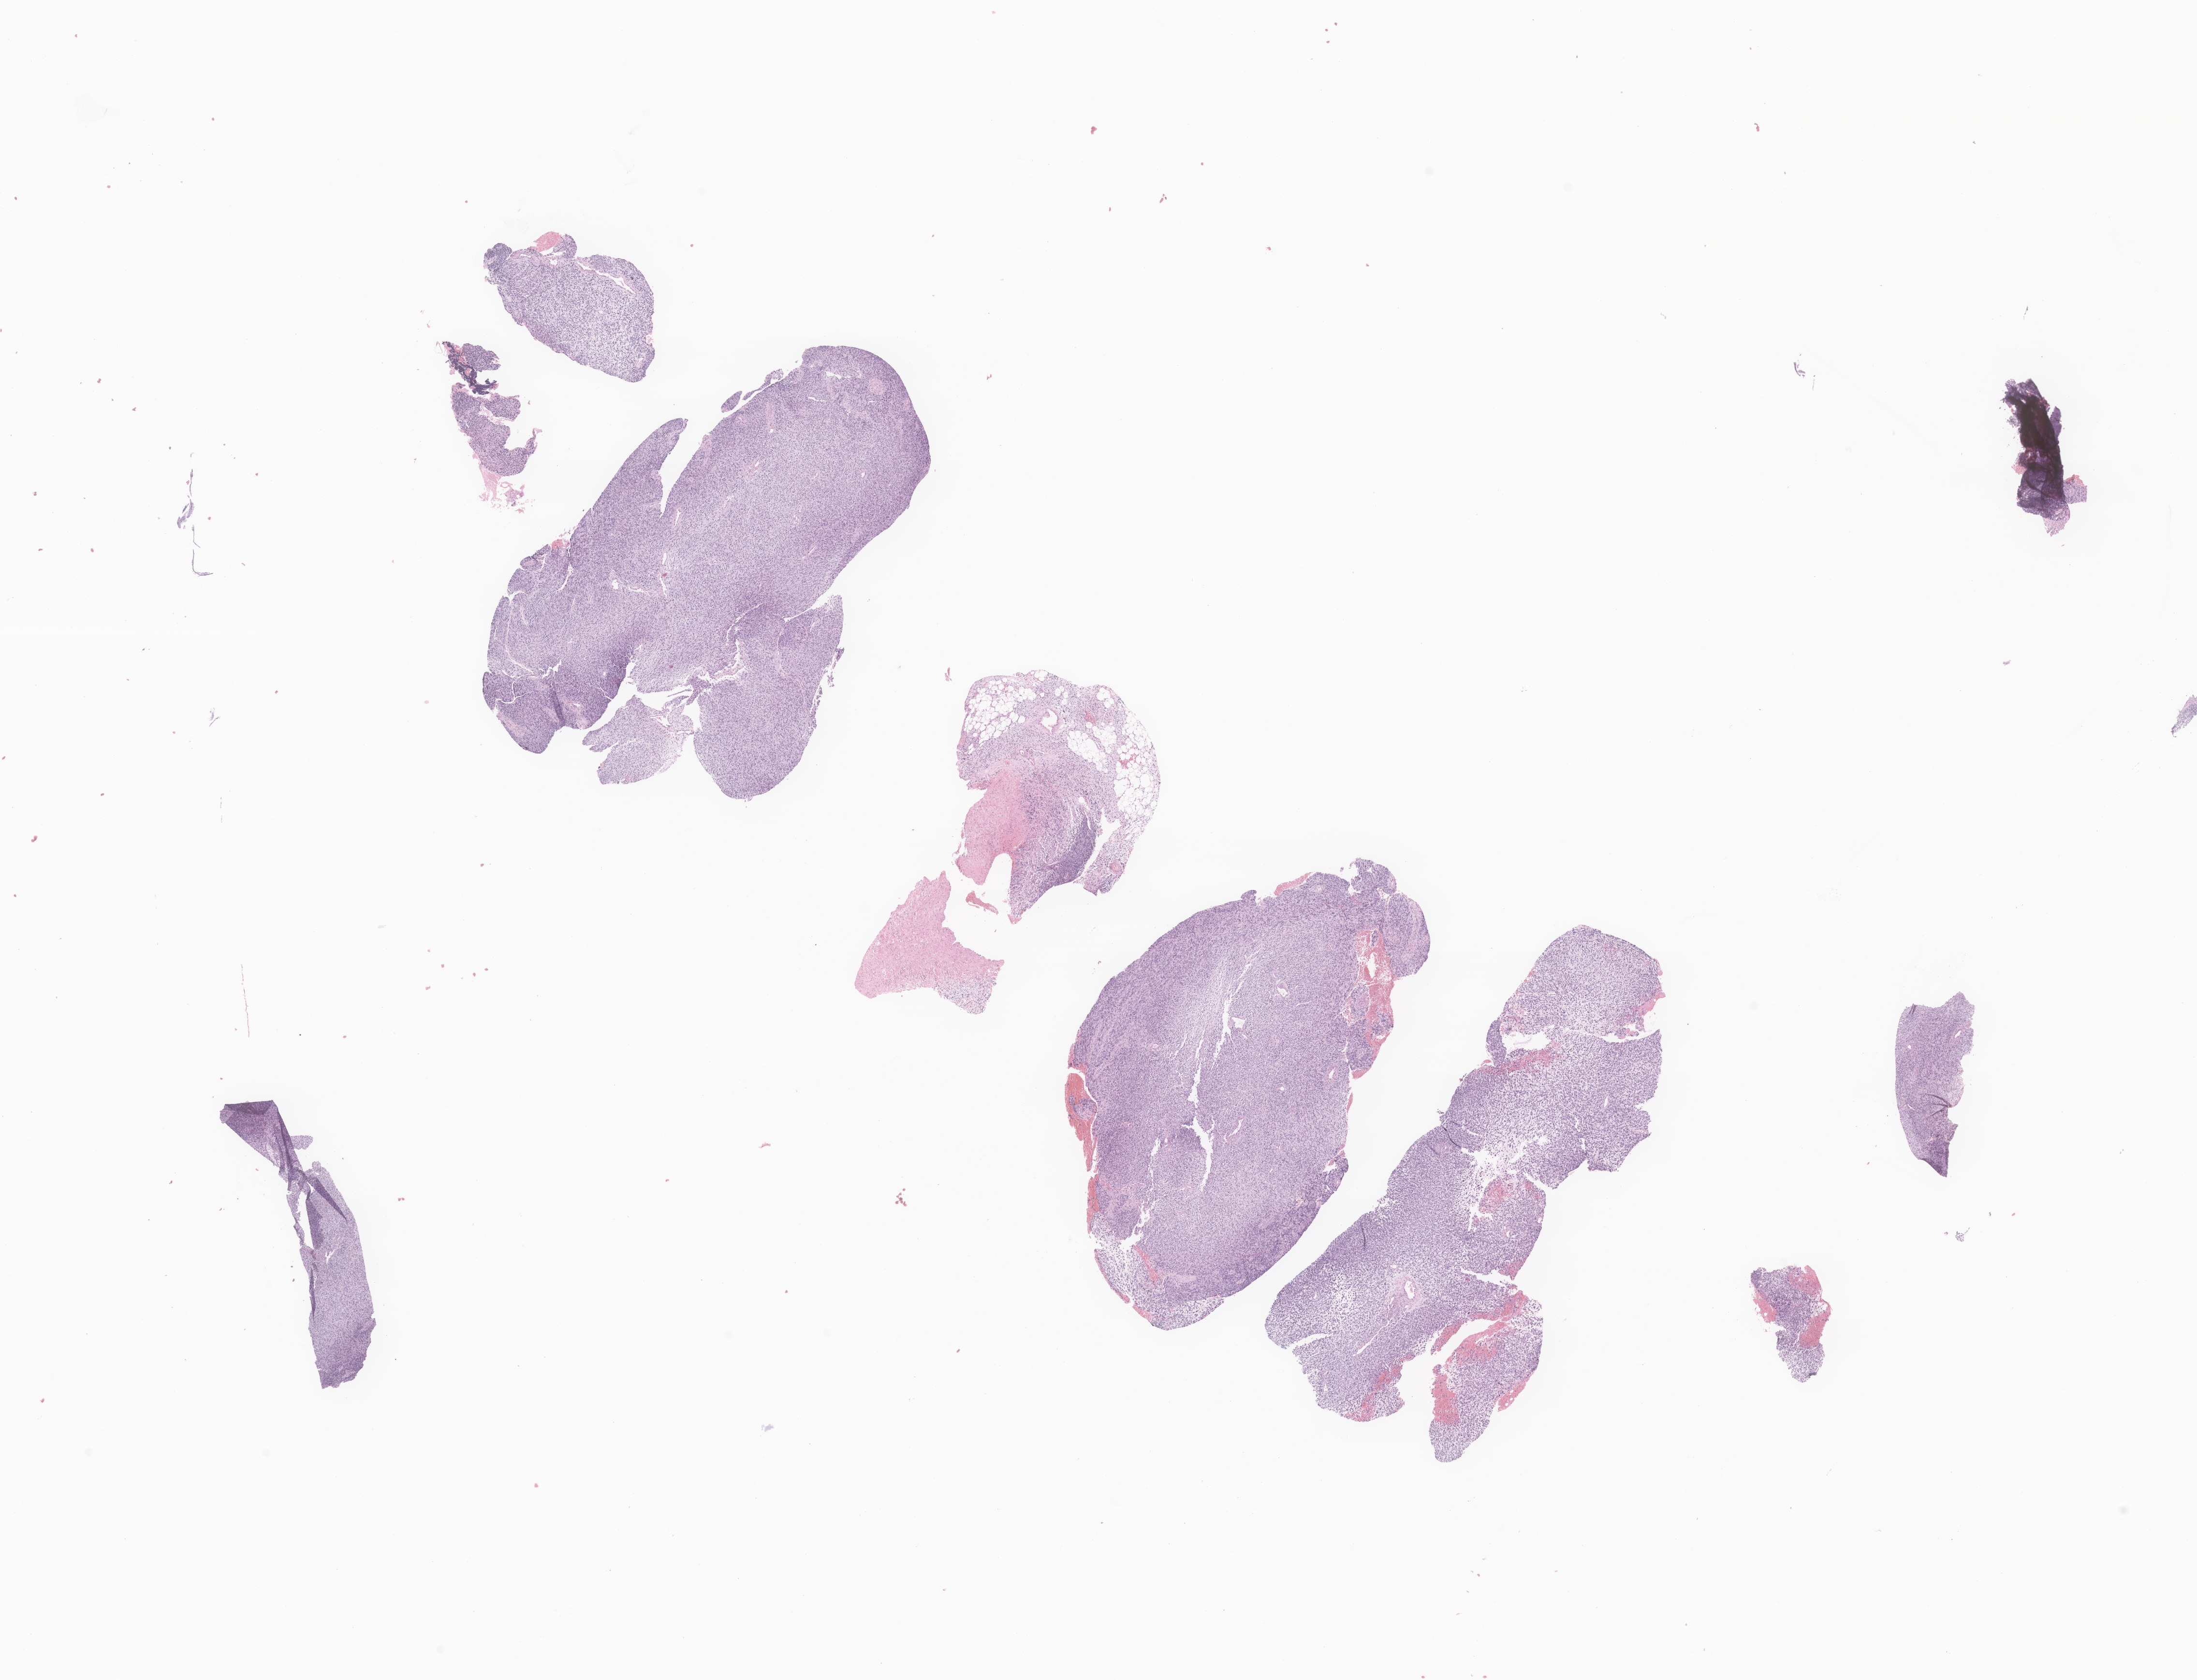
Haematoxylin and eosin whole-slide image of tumor tissue from the orbit, low-resolution overview of the scanned area, about 19.2 x 14.7 mm; formalin-fixed, paraffin-embedded (FFPE) tissue. Male patient, age 63 months (5 years 3 months).
Diagnosis (ICD-O-3 morphology term): Embryonal rhabdomyosarcoma, NOS.